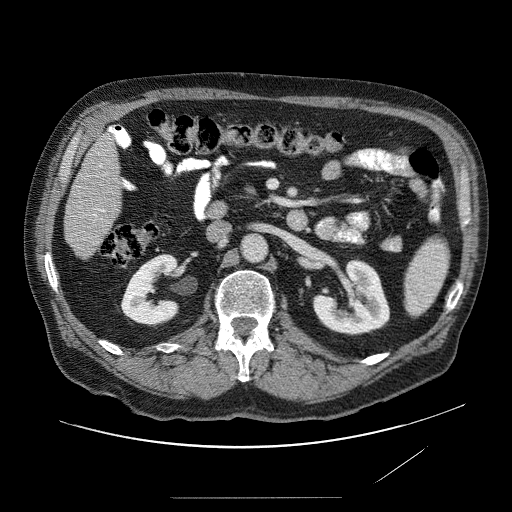
Contrast-enhanced abdominal CT (liver protocol), one axial slice; reconstruction kernel STANDARD; 120 kVp; soft-tissue window (W 400 / L 40 HU); 2.5 mm slice thickness; 512 × 512 image matrix. From the clinical record (not read from this slice): diagnosis: hepatocellular carcinoma (patient treated with transarterial chemoembolisation; whether this scan precedes or follows treatment is not stated here); TNM stage (as recorded): Stage-IVA; Child-Pugh class: A; tumour differentiation: moderately differentiated.
Outlined on this slice (semi-automatic segmentation, software-assisted and operator-edited):
- liver parenchyma outside the tumour (the mass and vessels are separate outlines, so this box may not span the whole liver): bounding box <62,128,130,264> (left, top, right, bottom; pixels)
- liver vessels: <101,165,117,219>